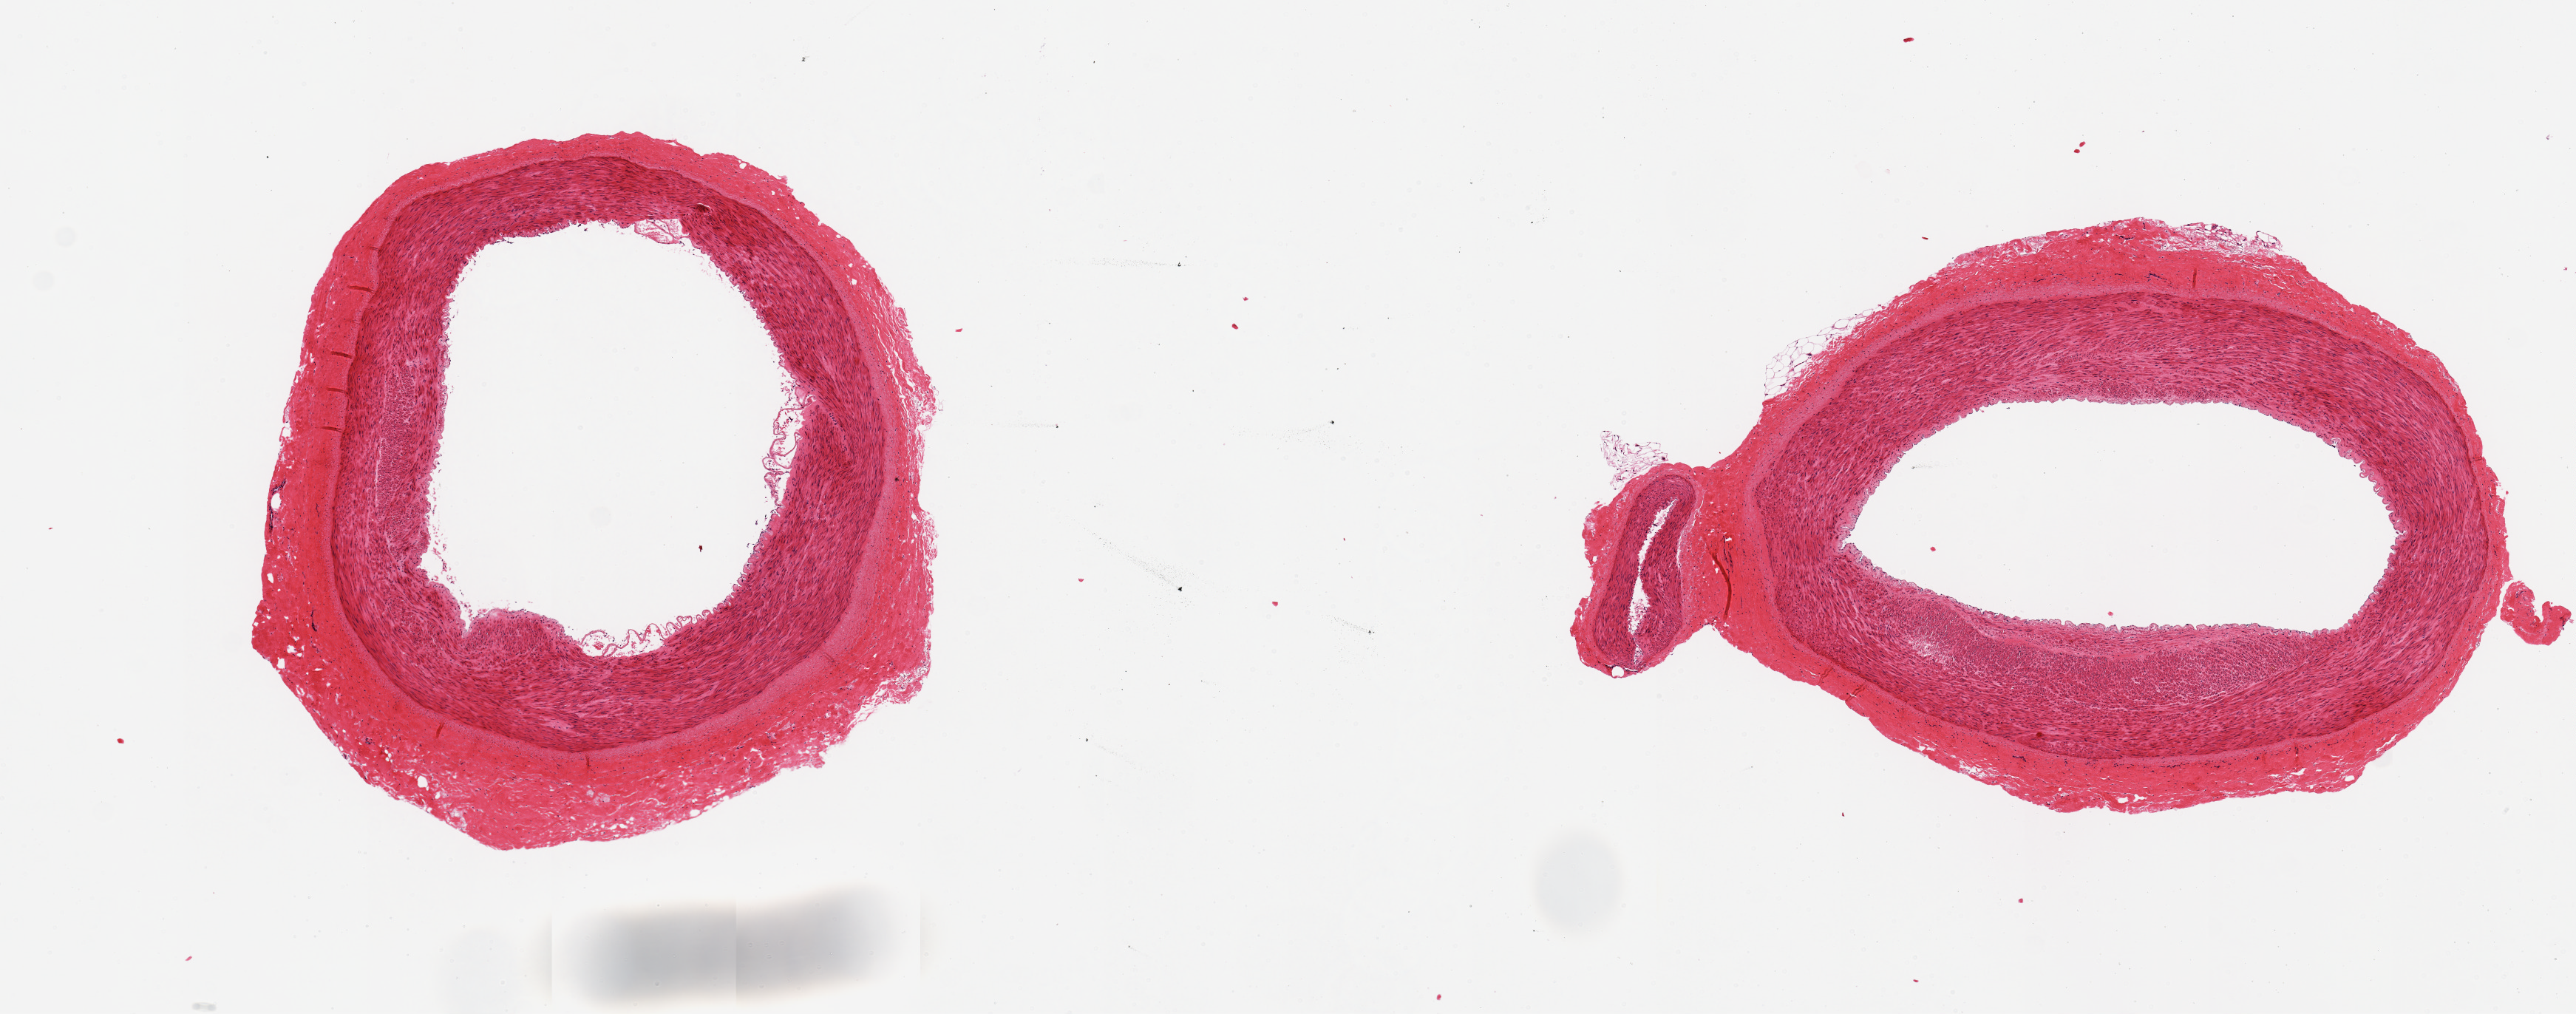
Haematoxylin and eosin whole-slide image, brightfield, whole scanned area (about 13.8 x 5.4 mm) shown as a low-resolution overview. PAXgene-fixed paraffin-embedded (PFPE) section. Sampled site (target tissue): tibial artery. Tissue donor sample. Donor sex: female.
Reviewer comment on this tissue sample: 2 pieces, well trimmed.